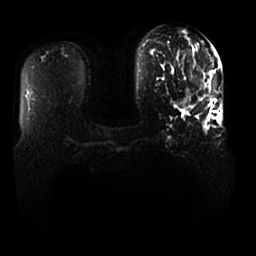
Breast MRI, one axial slice. Slice 6 of 25 in the series (ordered by position). Diffusion-weighted series; image 2 of 4 stored at this slice position (different b-values; order by instance number). 1.5 T. 4 mm slice thickness. 256 × 256 image matrix, field of view 370 × 370 mm. Female patient.
Structures marked on this image (outlined manually by an expert reader):
- tumour on diffusion-weighted imaging: bounding box (x1, y1, x2, y2) in pixels: (176, 99, 191, 107)